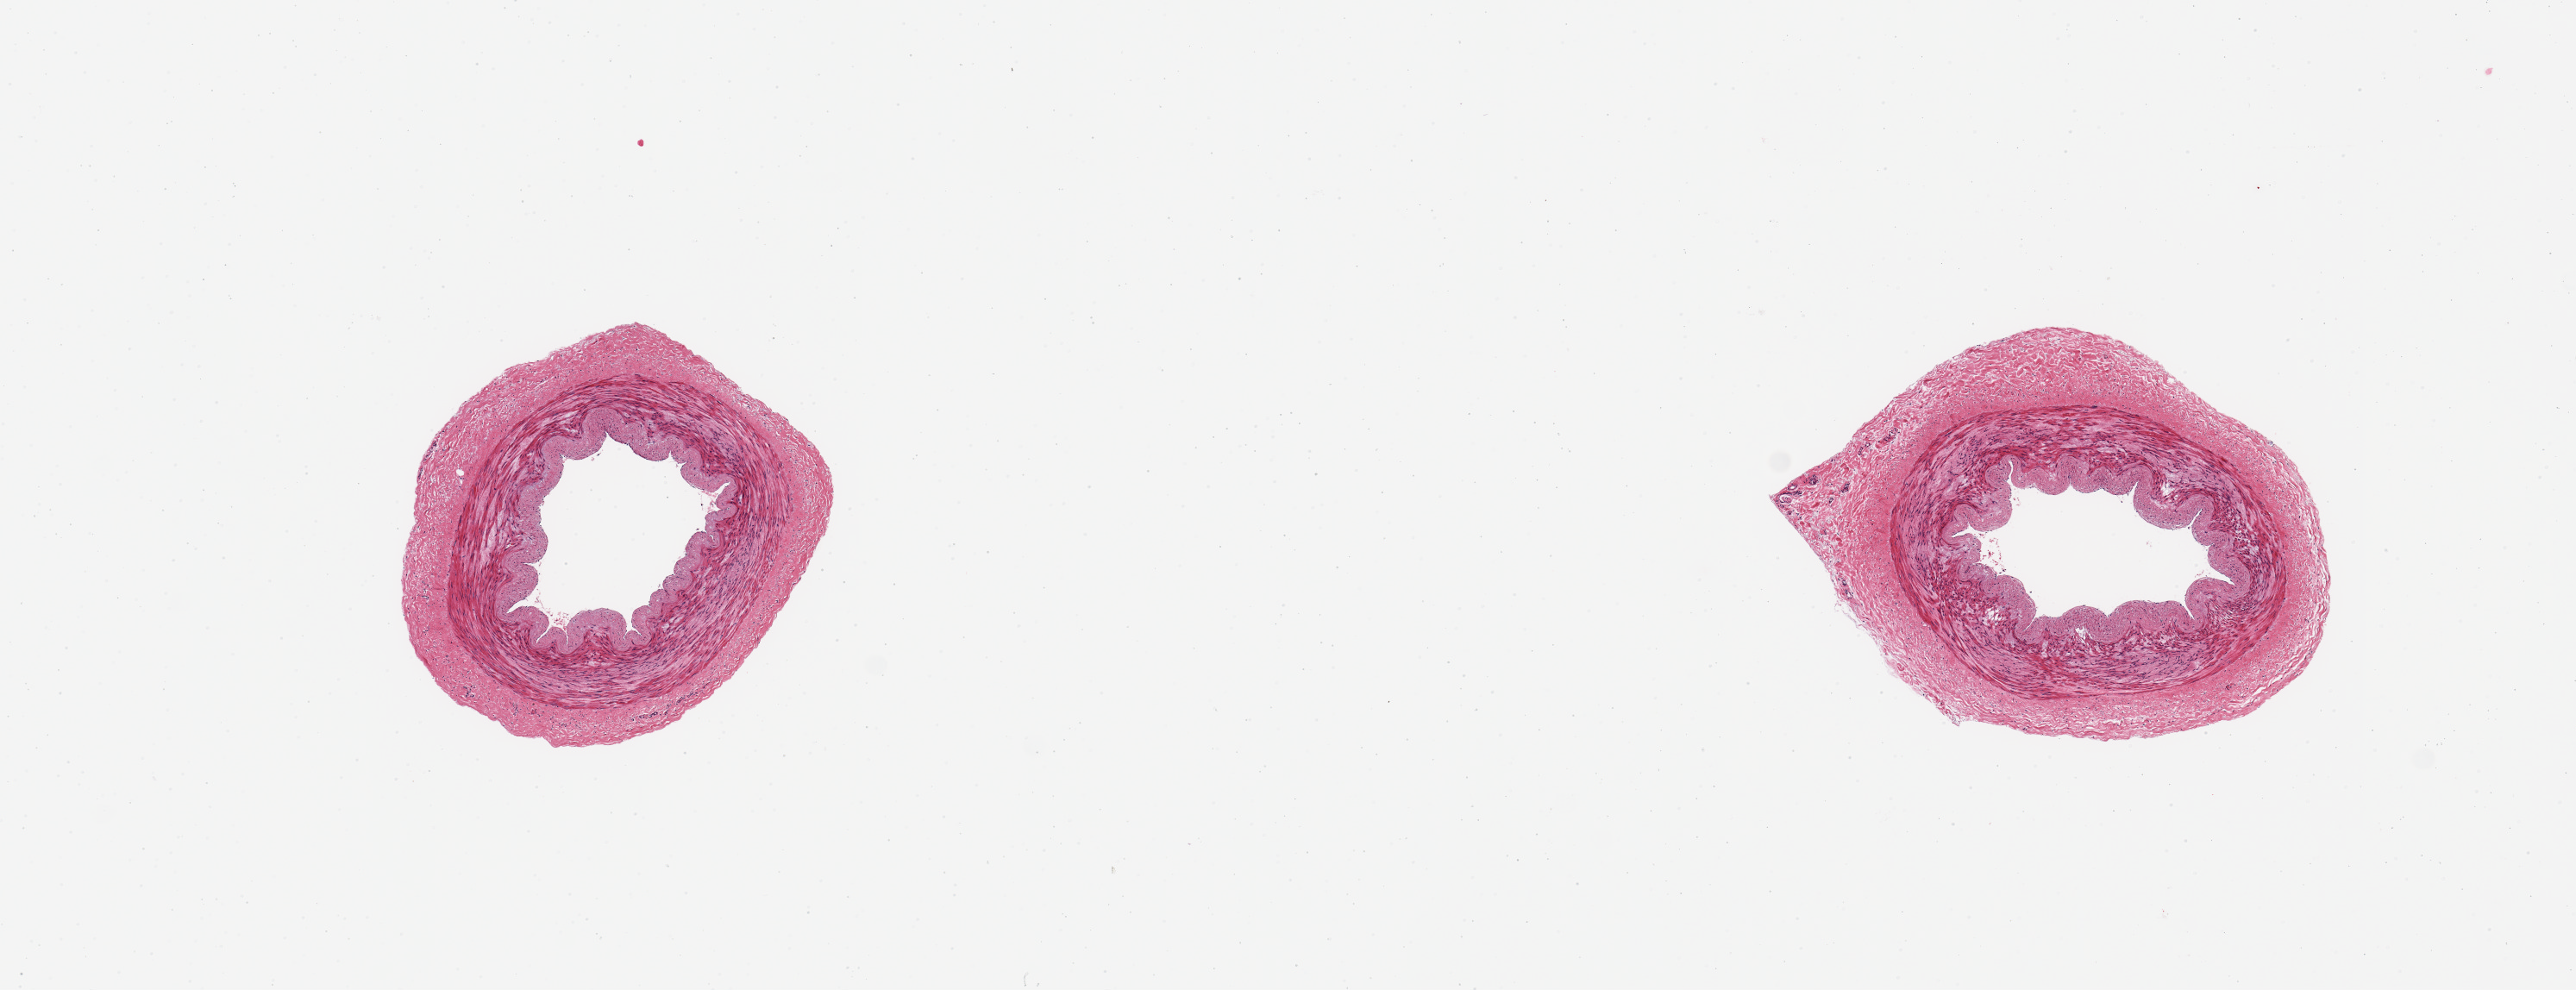
Hematoxylin and eosin (H&E) whole-slide image, low-resolution overview of the scanned area, about 11.8 x 4.5 mm. PAXgene-fixed paraffin-embedded (PFPE) section. Sampled site (target tissue): tibial artery. Tissue donor sample.
Pathologist's review note for this sample: 2 pieces; minimal plaque; well trimmed.